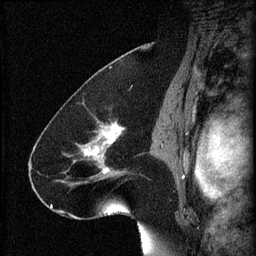
Breast MRI (dynamic contrast-enhanced), one sagittal slice; position 40 of 60 along the scan axis; 3 images stored at this slice position (order not interpretable as contrast timing); 1.5 T; TE 4.2 ms, TR 8.2 ms; 2 mm slice thickness; 256 × 256 image matrix, field of view 180 × 180 mm. Female patient, age 41 years.
Outlined on this slice (semi-automatic segmentation, software-assisted and operator-edited):
- analysis volume of interest (the breast-tissue region the enhancement analysis was run in; not a lesion): bounding box <72,122,132,189> (left, top, right, bottom; pixels)
- tumour enhancement mask (voxels above the 70 % enhancement threshold inside the analysis volume of interest): <79,122,124,185>